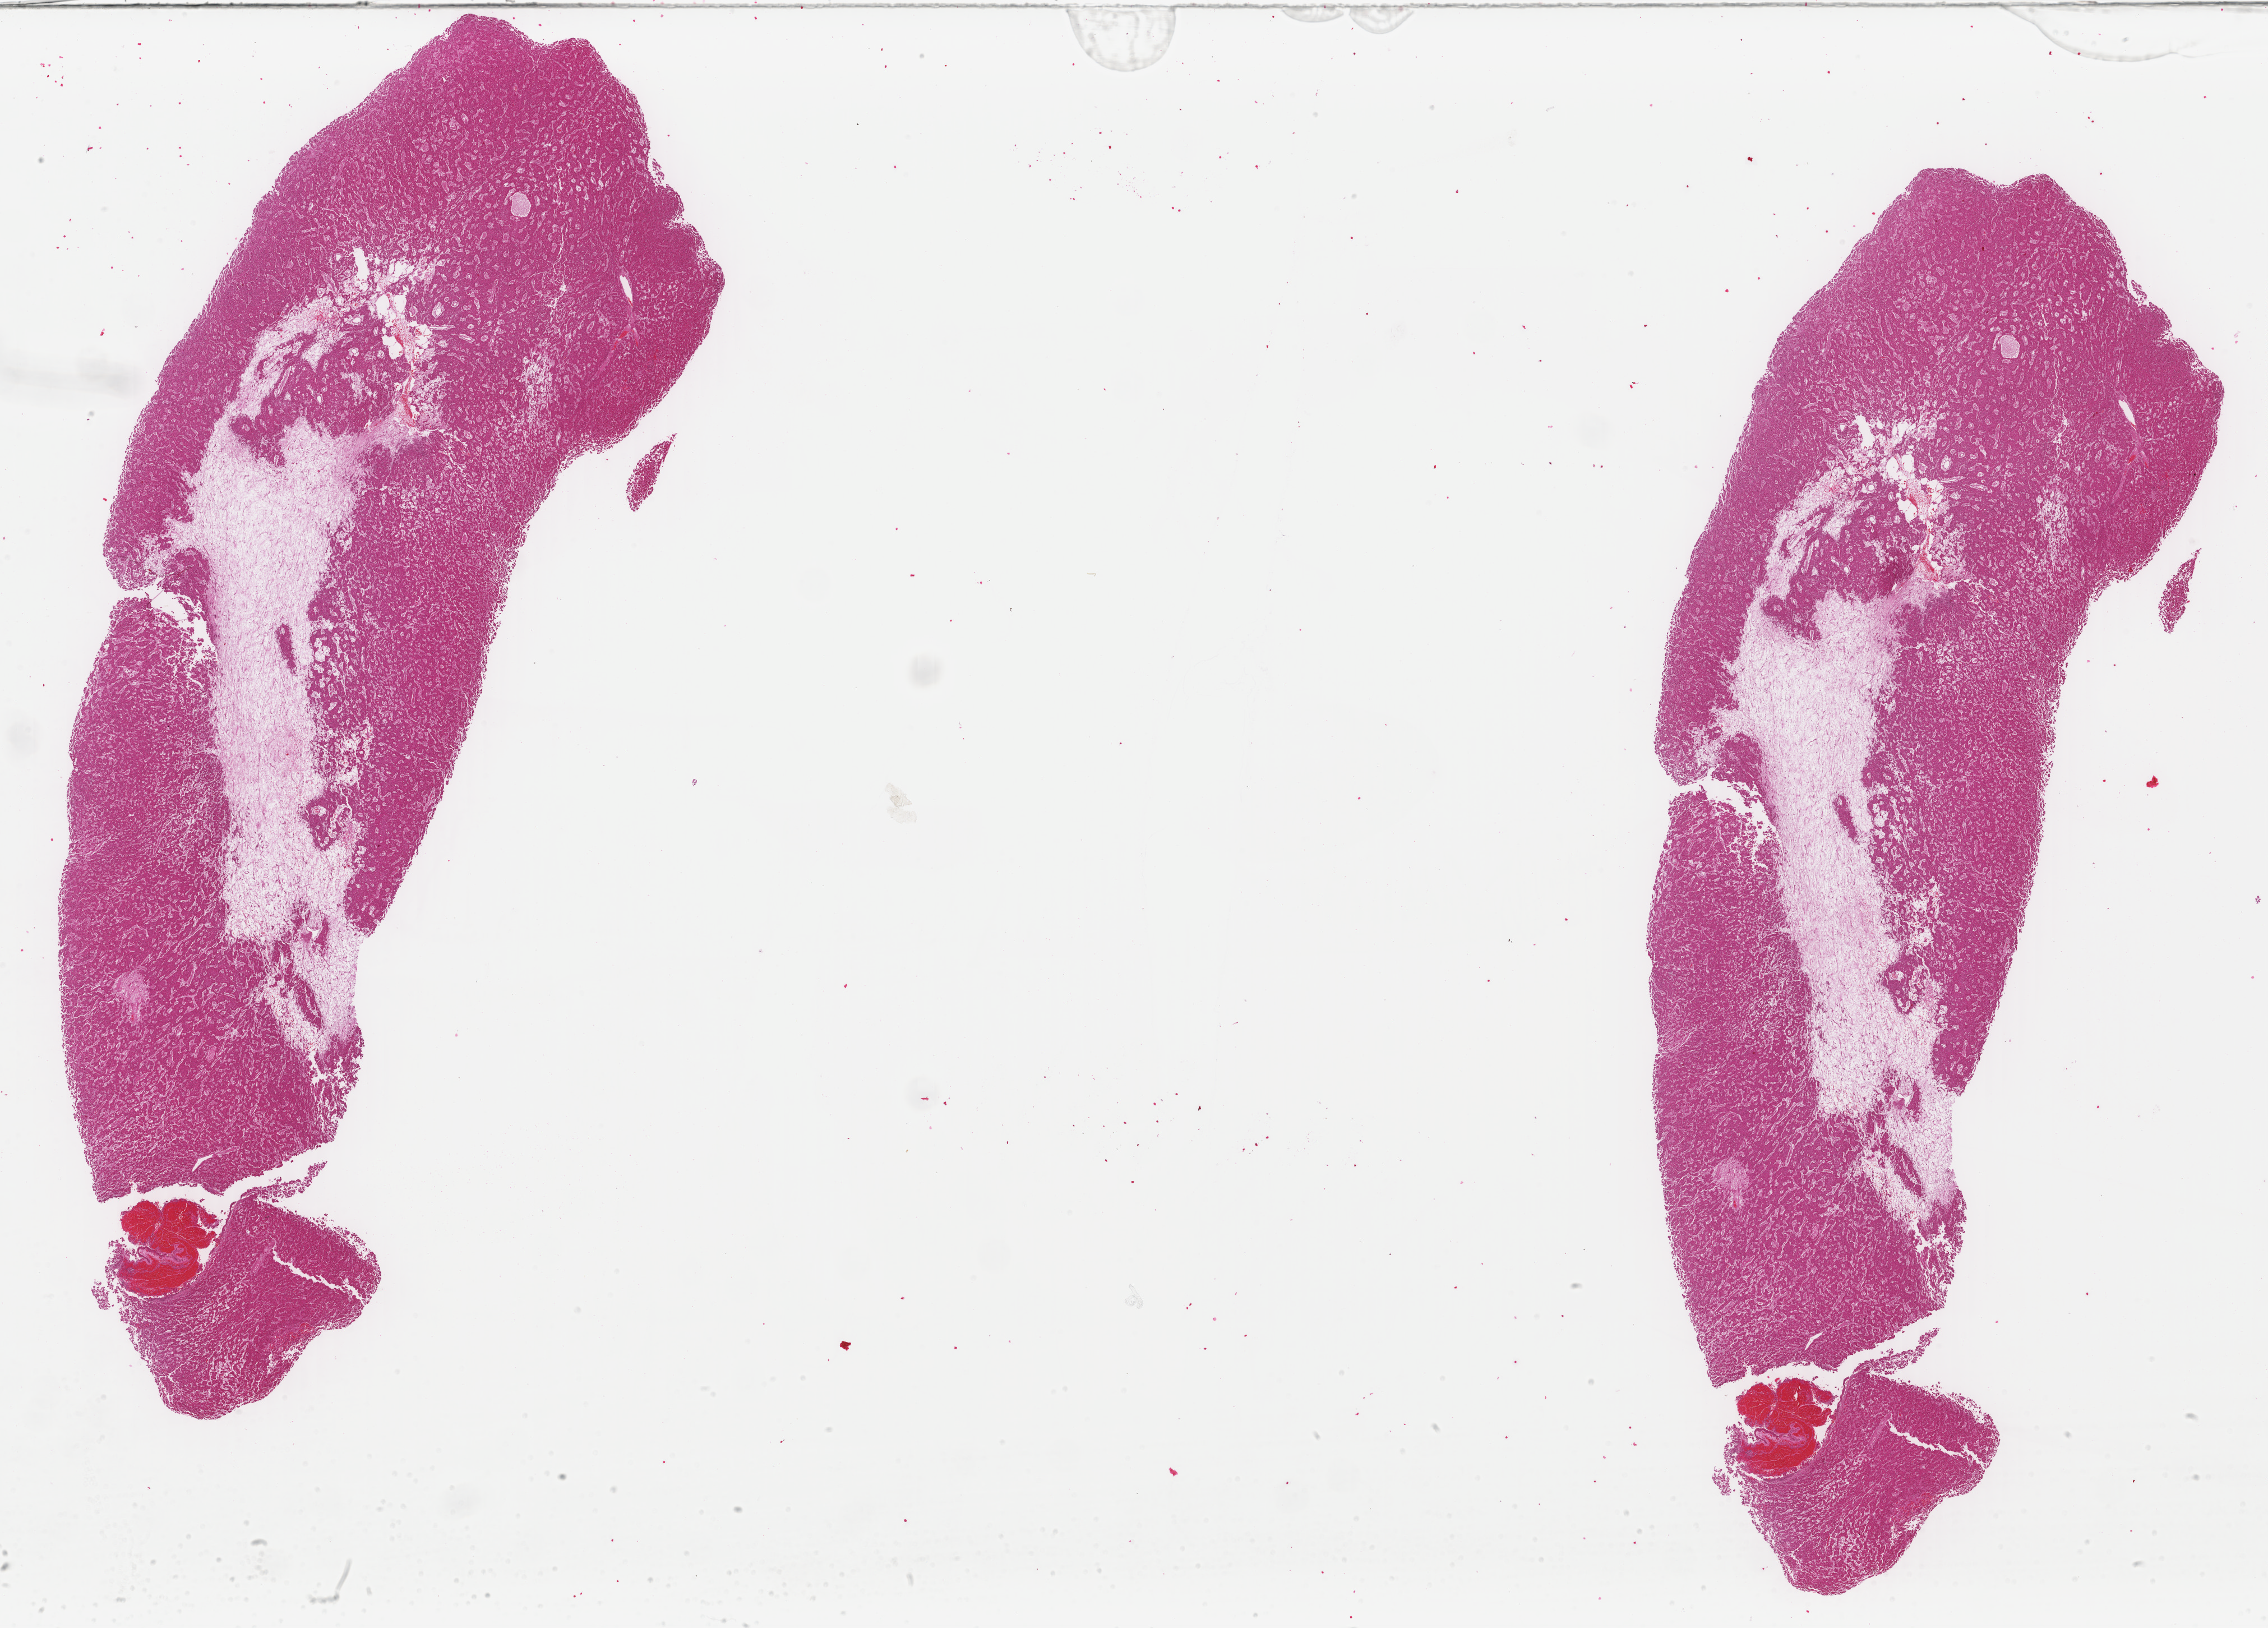
H&E whole-slide image — a low-resolution overview of the entire scanned area, about 32.1 x 23.0 mm (acquisition: 40x scan). Formalin-fixed paraffin-embedded (FFPE) diagnostic section. Primary tumour sample from the liver. Male patient; age at initial diagnosis 76 years. Histologic grade: G1 (well differentiated).
Pathologic diagnosis: Hepatocellular carcinoma, NOS.